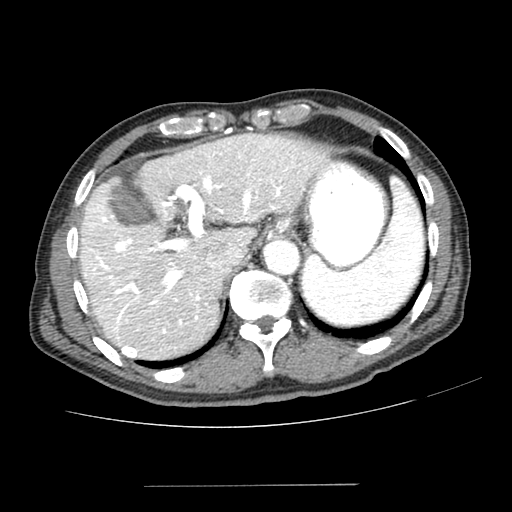
Contrast-enhanced abdominal CT (liver protocol), one axial slice; slice 166 of 187 in the series (ordered by position); reconstruction kernel SOFT; 100 kVp; one of 2 acquisitions stored at this slice position; soft-tissue window (W 400 / L 40 HU); 512 × 512 image matrix. From the clinical record (not read from this slice): diagnosis: hepatocellular carcinoma (patient treated with transarterial chemoembolisation; whether this scan precedes or follows treatment is not stated here); TNM stage (as recorded): Stage-I; Child-Pugh class: A.
Outlined on this slice (semi-automatic segmentation, software-assisted and operator-edited):
- liver parenchyma outside the tumour (the mass and vessels are separate outlines, so this box may not span the whole liver): bounding box (x1, y1, x2, y2) in pixels: (80, 134, 331, 360)
- liver vessels: (85, 140, 307, 352)